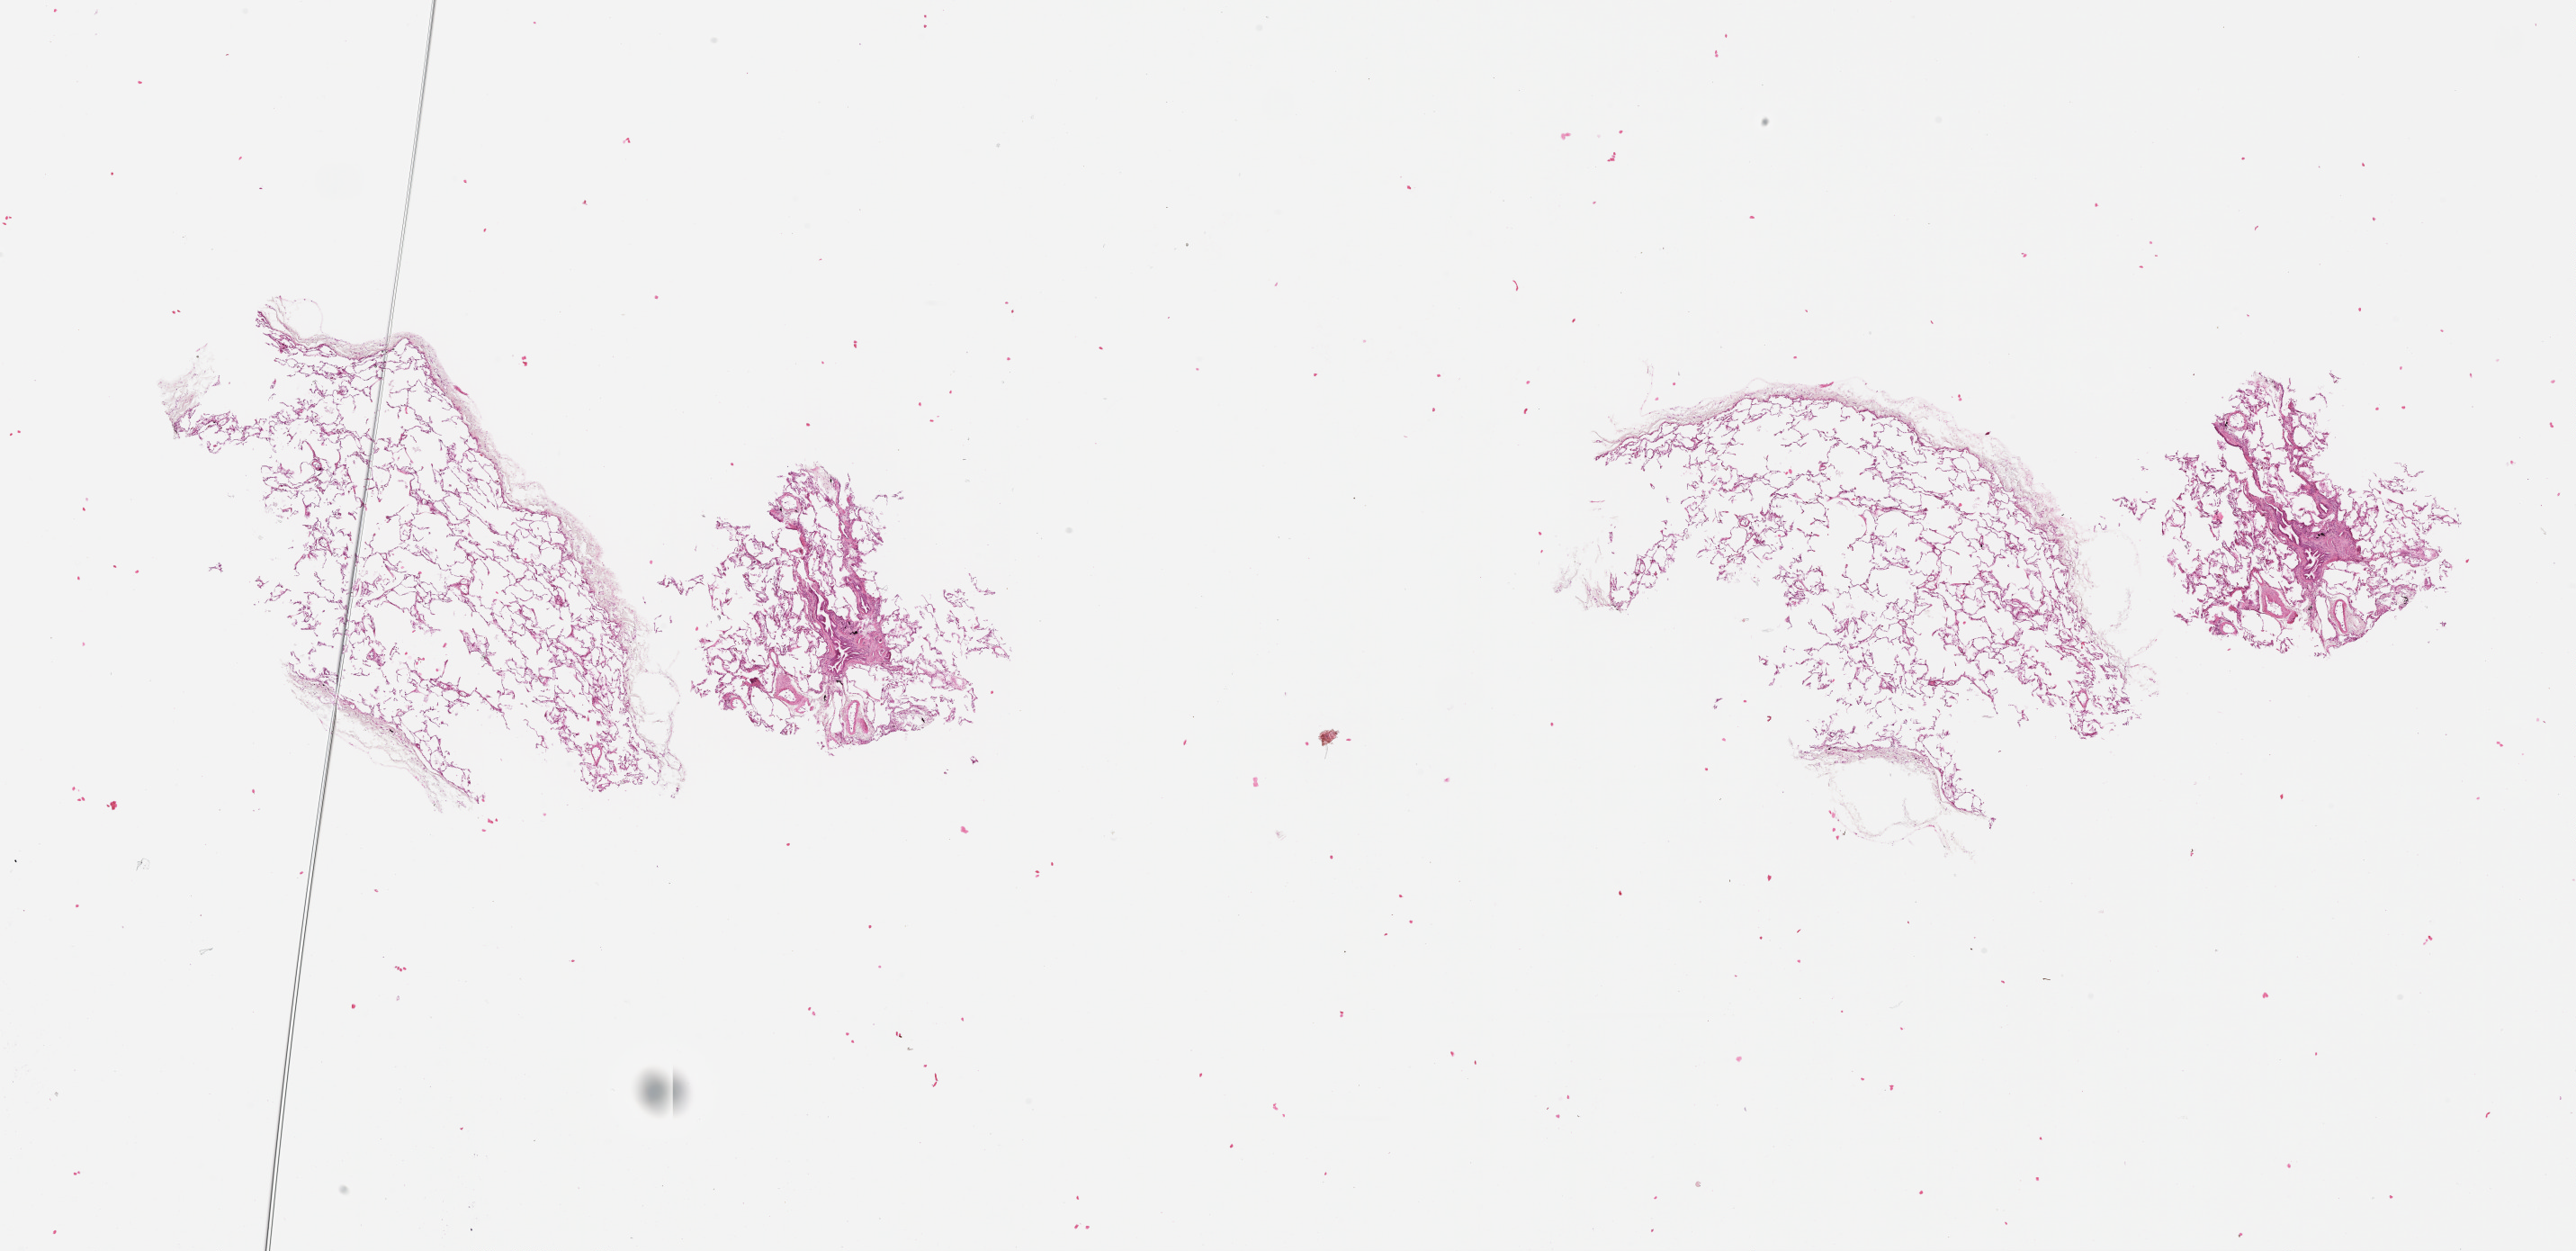
H&E whole-slide image — shown as a low-resolution overview of the whole scanned area (about 23.1 x 11.2 mm, acquisition: 20x scan), lung, normal (non-tumour) tissue. Male, 55 y/o.
This section: normal (non-tumour) tissue from the same patient. Patient diagnosis (cohort enrolment): squamous cell carcinoma (lung).